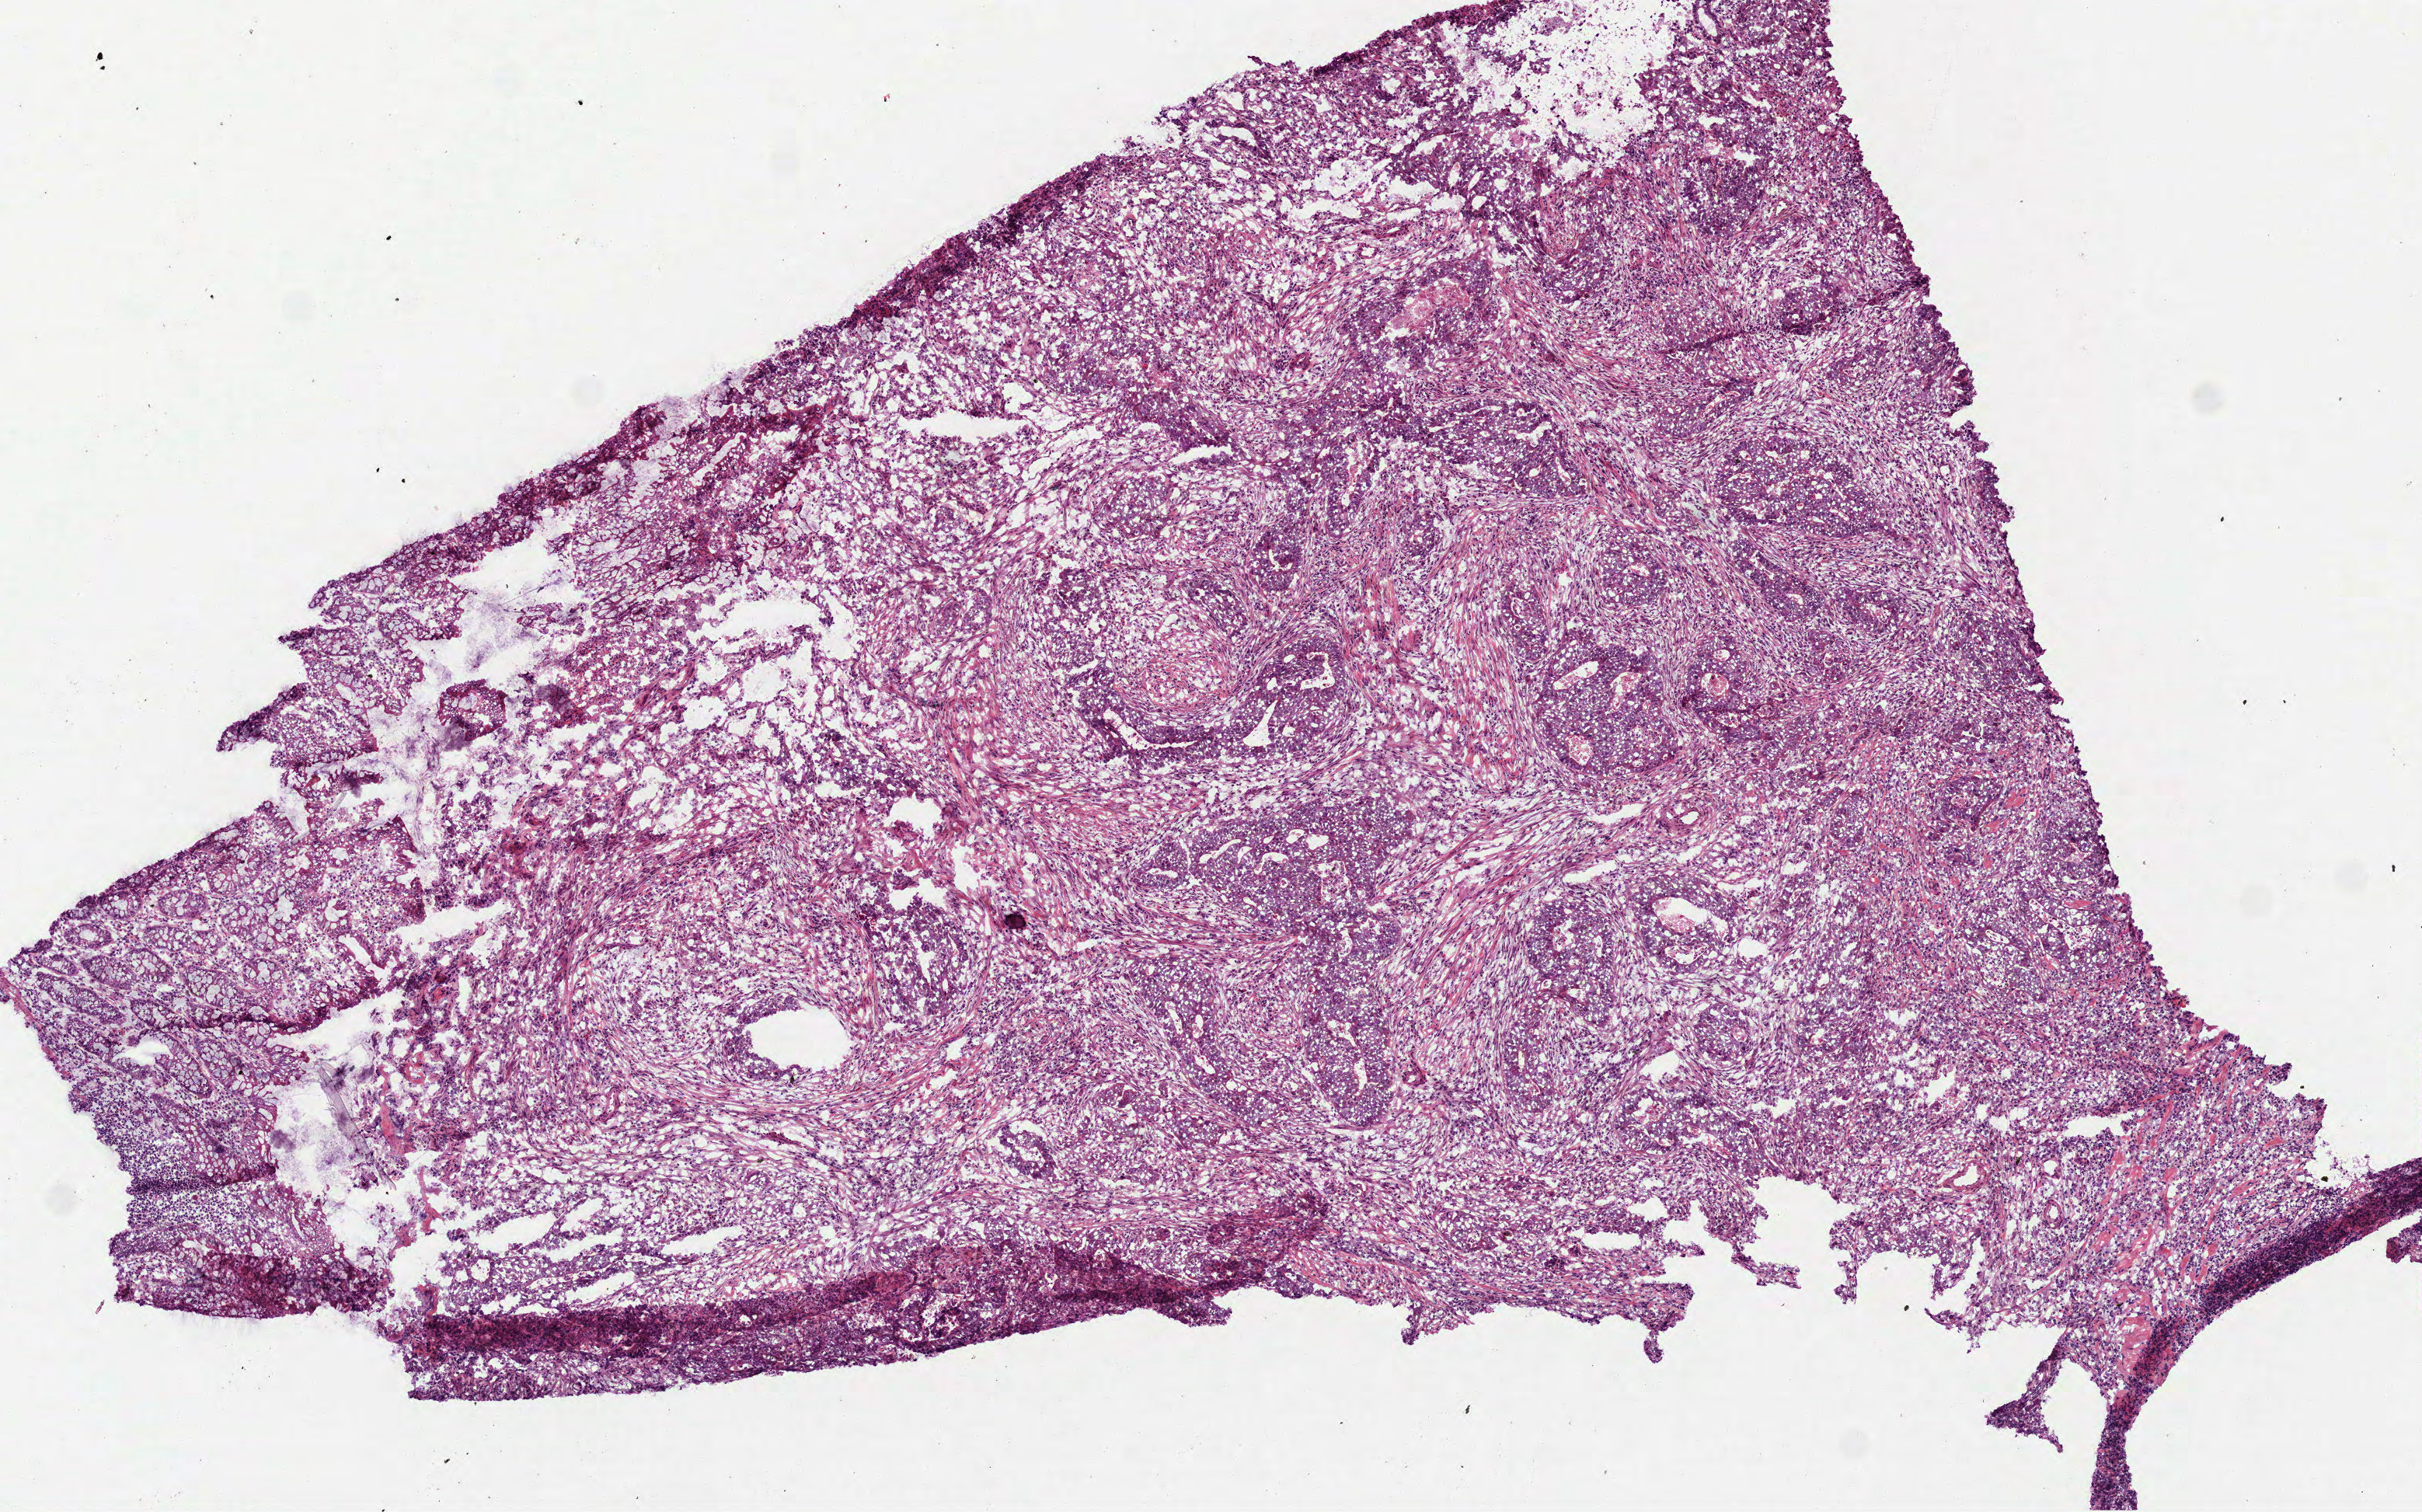
H&E whole-slide image, shown as a low-resolution overview of the whole scanned area (about 6.3 x 3.9 mm, slide scanned at 40x); frozen section from the top of the tissue portion; primary tumour sample from the colon. Patient: male, age at initial diagnosis 77 years. Pathologist review of this section (percent, as recorded): tumour cells 72%, tumour nuclei 60%, normal cells 10%, stromal cells 15%, necrosis 3%.
TNM: T4 N1 M0. Pathologic diagnosis: Adenocarcinoma, NOS (ascending colon). Lymph nodes positive (case pathology): 1 of 22 examined. AJCC pathologic stage: IIIB (6th edition).